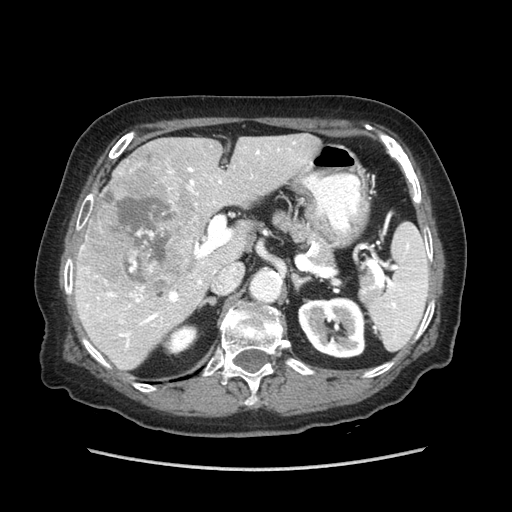
Contrast-enhanced abdominal CT (liver protocol), one axial slice; reconstruction kernel STANDARD; 140 kVp; soft-tissue window (W 400 / L 40 HU); 512 × 512 image matrix, field of view 360 × 360 mm. Case-level facts recorded for this patient, not image findings: diagnosis: hepatocellular carcinoma (patient treated with transarterial chemoembolisation; whether this scan precedes or follows treatment is not stated here); TNM stage (as recorded): Stage-IIIA; Child-Pugh class: A; tumour differentiation: well differentiated; tumour nodularity: multinodular.
Outlined on this slice (semi-automatically segmented with operator editing):
- liver parenchyma outside the tumour (the mass and vessels are separate outlines, so this box may not span the whole liver): bounding box <74,134,318,370> (left, top, right, bottom; pixels)
- mass: <82,162,199,296>
- liver vessels: <86,142,295,347>